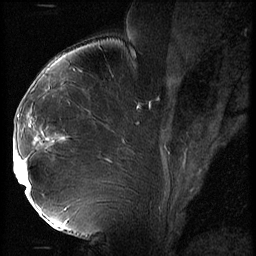
Breast MRI (dynamic contrast-enhanced), one sagittal slice; slice 35 of 56 in the series (ordered by position); 3 images stored at this slice position (order not interpretable as contrast timing); 1.5 T; TE 4.2 ms, TR 9 ms; 2.5 mm slice thickness; 256 × 256 image matrix, field of view 180 × 180 mm. Female patient, age 43 years. Case-level facts recorded for this patient, not image findings: setting: breast cancer imaged before/during neoadjuvant chemotherapy; receptor status: HER2-positive.
Outlined on this slice (semi-automatic segmentation, software-assisted and operator-edited):
- analysis volume of interest (the breast-tissue region the enhancement analysis was run in; not a lesion): bounding box (x1, y1, x2, y2) in pixels: (14, 92, 74, 211)
- tumour enhancement mask (voxels above the 140 % enhancement threshold inside the analysis volume of interest): (14, 143, 30, 198)